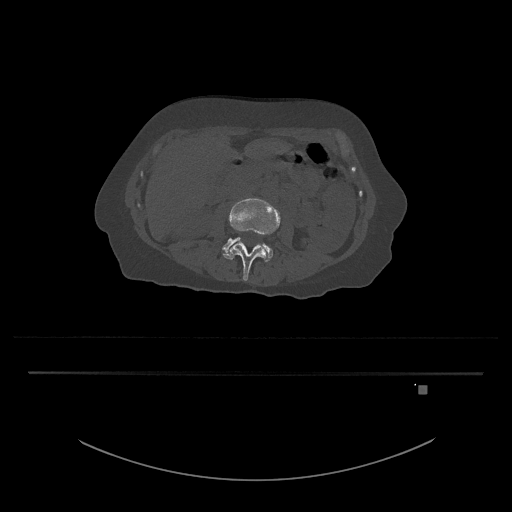
CT including the spine, one axial slice; slice 408 of 797 in the series (ordered by position); 120 kVp; bone window (W 1800 / L 400 HU); 0.5 mm slice thickness; 512 × 512 image matrix, field of view 500 × 500 mm. Female patient, age 57 years. Case-level facts recorded for this patient, not image findings: primary cancer: cervical.
Outlined on this slice (semi-automatic segmentation, software-assisted and operator-edited):
- L3 vertebra: bounding box <223,198,281,281> (left, top, right, bottom; pixels)
- L4 vertebra: <222,237,273,262>